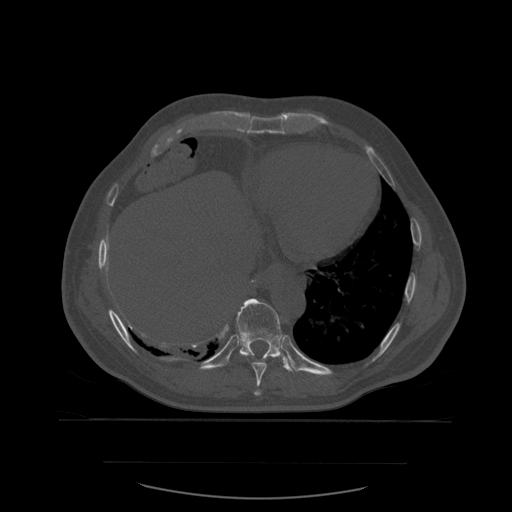
CT including the spine, one axial slice; position 329 of 590 along the scan axis; bone window (W 1800 / L 400 HU); 512 × 512 image matrix. Patient age 71 years. From the clinical record (not read from this slice): primary cancer: lung; vertebrae with lytic lesions (as recorded): T1, T2, L5, S1.
Outlined on this slice (semi-automatically segmented with operator editing):
- T10 vertebra: box from (x=236, y=299) to (x=298, y=372) px
- T9 vertebra: (x=252, y=358)–(x=267, y=396)